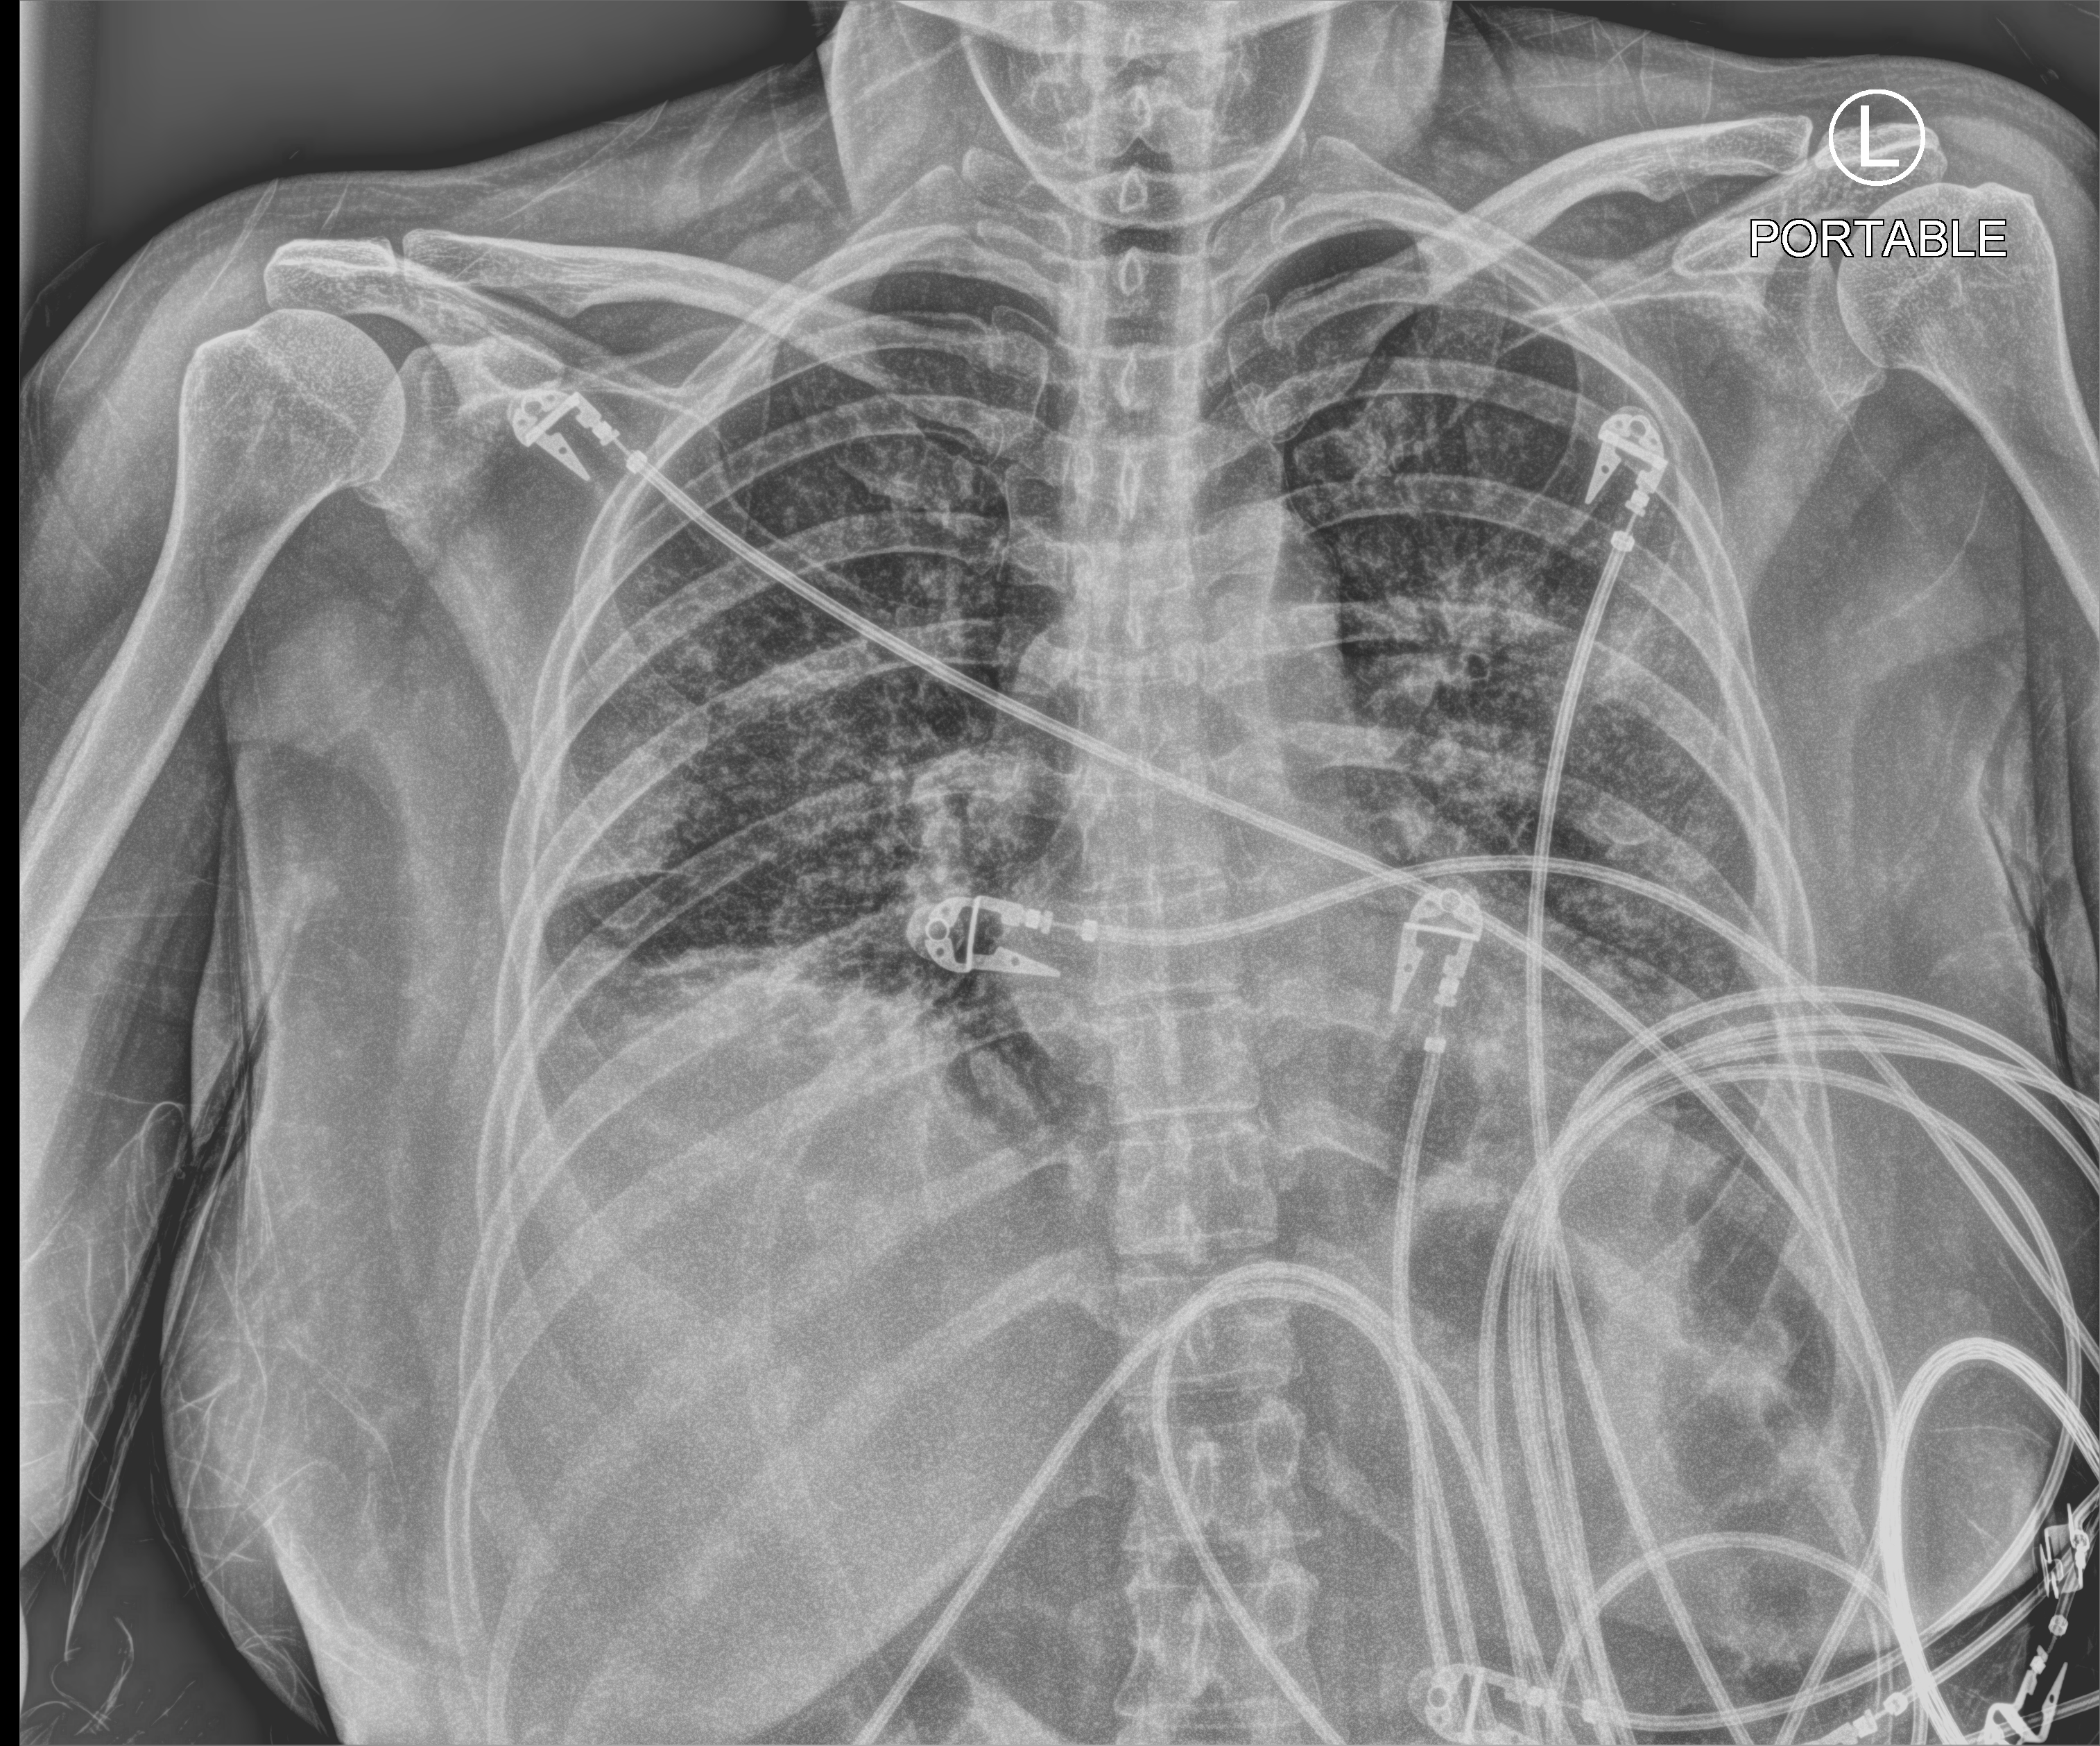
Portable chest radiograph, anteroposterior (AP) projection. Patient hospitalised with COVID-19; female, aged 18–59 years.
Hospital-stay facts (about this admission, not read from this image; timing relative to this image not recorded): admitted to intensive care during this hospital stay: yes; mechanically ventilated during this hospital stay: no; other chronic lung disease (admission record): no.